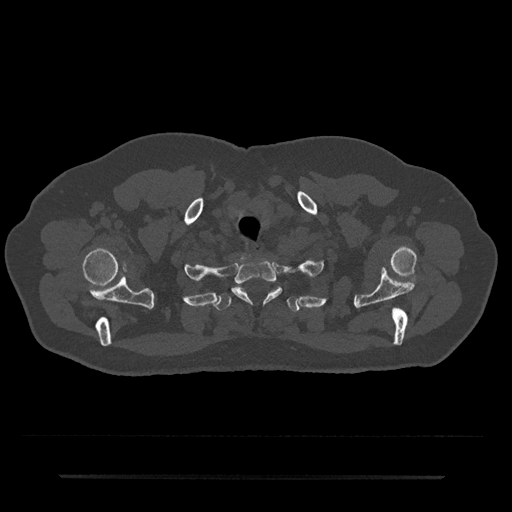
CT including the spine, one axial slice. Slice 631 of 797 in the series (ordered by position). 120 kVp. Bone window (W 1800 / L 400 HU). 0.5 mm slice thickness. 512 × 512 image matrix, field of view 437 × 437 mm. Male patient, age 69 years. Case-level facts recorded for this patient, not image findings: primary cancer: prostate.
Annotated regions visible in this slice (semi-automatically segmented with operator editing):
- T1 vertebra: box from (x=232, y=260) to (x=282, y=303) px
- T2 vertebra: (x=216, y=287)–(x=300, y=312)